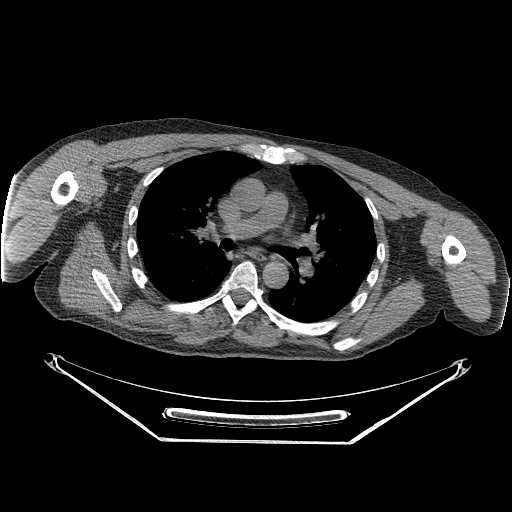
CT of an extremity soft-tissue mass (from a PET/CT study), one axial slice; slice 178 of 267 in the series (ordered by position); soft-tissue window (W 400 / L 40 HU); 3.75 mm slice thickness; 512 × 512 image matrix, field of view 500 × 500 mm. Male patient. From the clinical record (not read from this slice): histological type: pleiomorphic spindle cell undifferentiated; grade: high; site of the primary tumour: right parascapusular.
Structures marked on this image (expert contour drawn on MRI and transferred to this co-registered scan by the dataset authors):
- gross tumour volume including surrounding oedema: bounding box (x1, y1, x2, y2) in pixels: (96, 294, 225, 334)